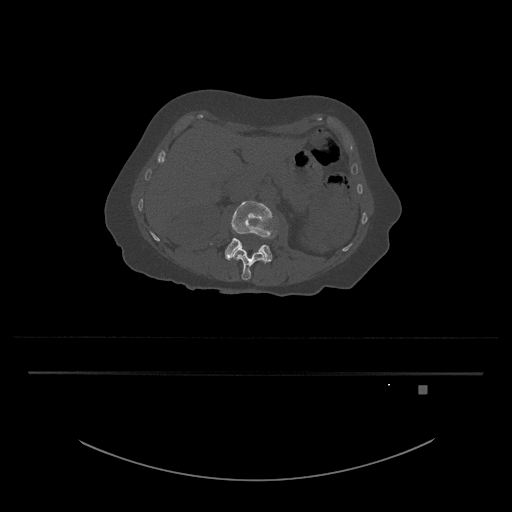
CT including the spine, one axial slice; position 459 of 797 along the scan axis; 120 kVp; bone window (W 1800 / L 400 HU); 512 × 512 image matrix. Patient: female, 57 years. Case-level facts recorded for this patient, not image findings: primary cancer: cervical.
Structures marked on this image (semi-automatic segmentation, software-assisted and operator-edited):
- L3 vertebra: box from (x=210, y=201) to (x=277, y=263) px